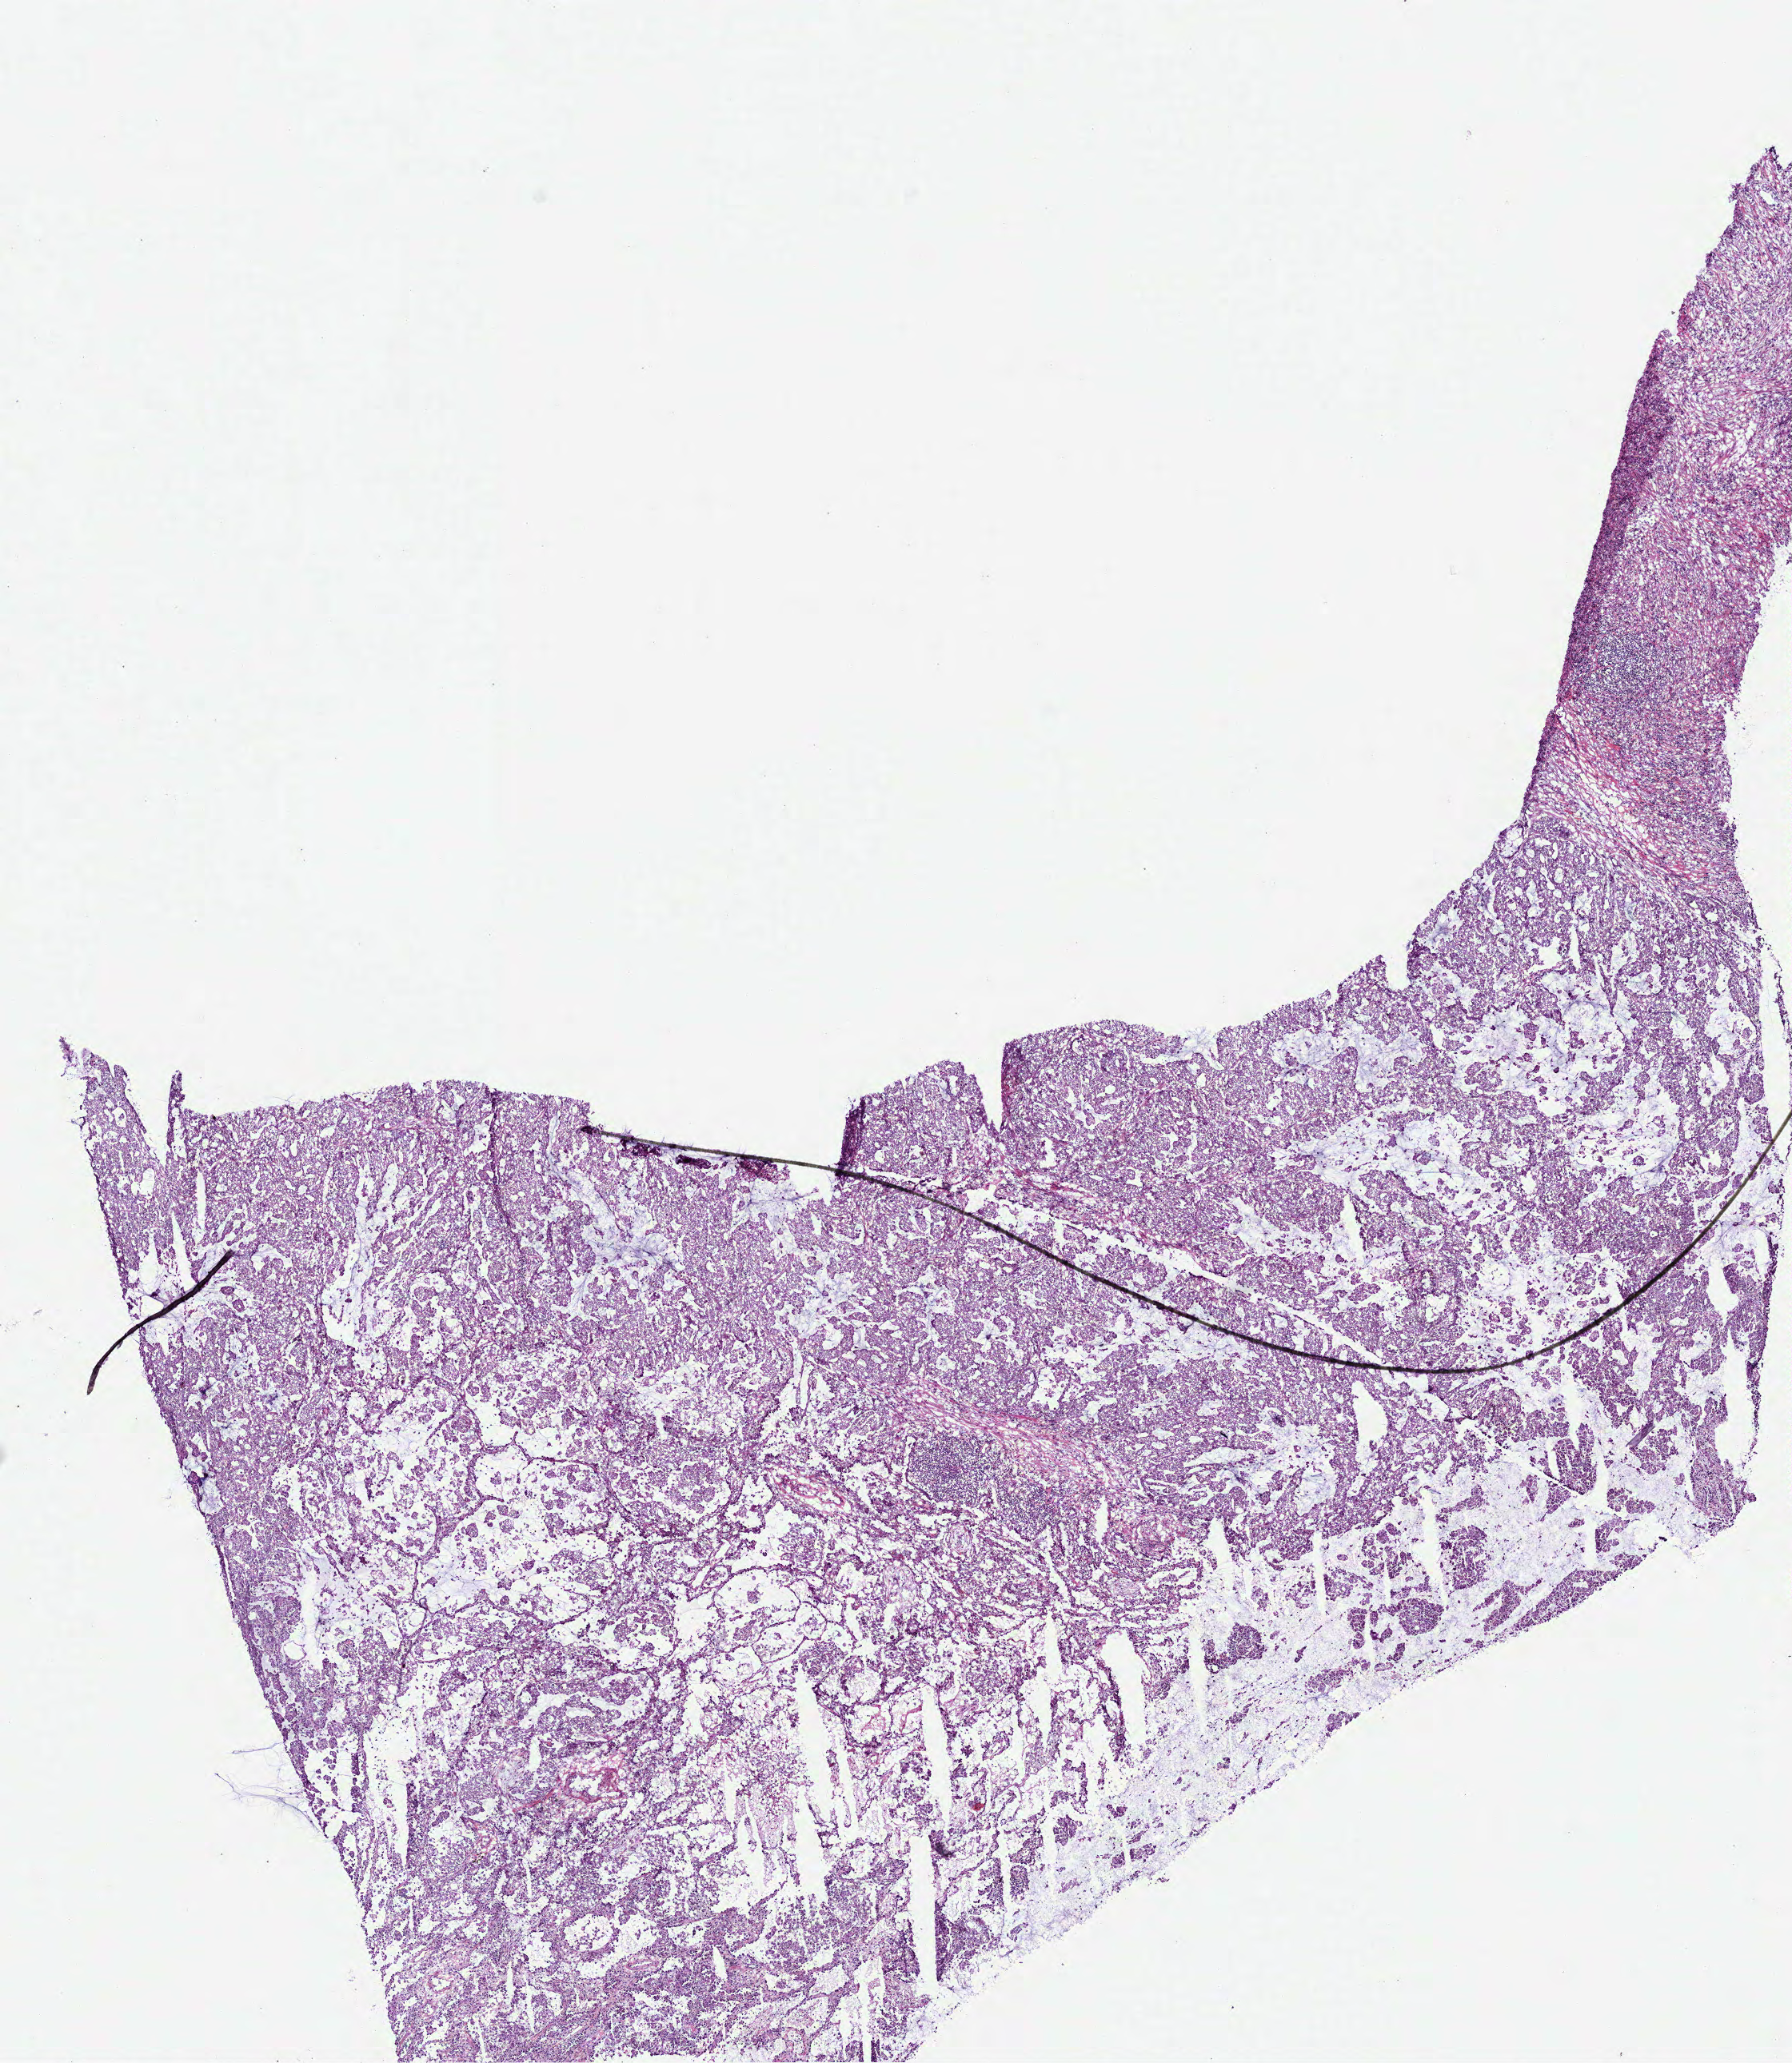
Whole-slide histology image, Hematoxylin and eosin (H&E) stained, whole scanned area (about 9.0 x 10.4 mm) shown as a low-resolution overview, frozen section from the bottom of the tissue portion, lung, primary tumour sample. Patient: male, age at initial diagnosis 58 years. Pathologist review of this section (percent, as recorded): tumour cells 93%, tumour nuclei 80%, normal cells 0%, stromal cells 7%, necrosis 0%. Inflammatory infiltration, as recorded: lymphocyte infiltration 10%, monocyte infiltration 5%, neutrophil infiltration 1%.
Diagnosis: Mucinous adenocarcinoma (lower lobe, lung). AJCC pathologic stage: IIIA (6th edition).